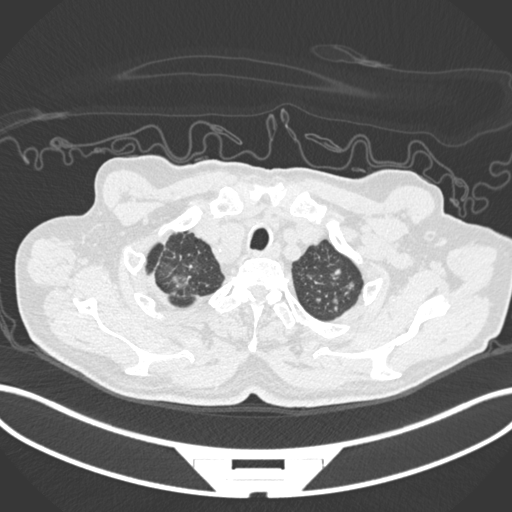
Chest CT, one axial slice; slice 201 of 207 in the series (ordered by position); reconstruction kernel B30f; 120 kVp; lung window (W 1500 / L -600 HU); 1 mm slice thickness; 512 × 512 image matrix, field of view 400 × 400 mm. Patient: male, 69 years. From the clinical record (not read from this slice): clinical TNM (as recorded): T1c N1 M1.
Structures marked on this image (bounding box drawn by a radiologist):
- lung tumour (recorded histology: adenocarcinoma): bounding box (x1, y1, x2, y2) in pixels: (169, 266, 193, 294)